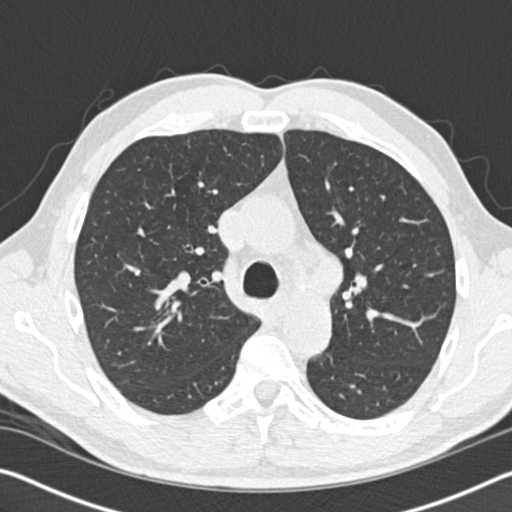
Axial slice from a low-dose chest CT screening exam; baseline annual screen; lung window (W 1500 / L -600 HU); standard (soft-tissue) reconstruction kernel (B30f); 512 × 512 image matrix, field of view 340 × 340 mm. Male participant, aged 61 years at enrolment. Former smoker at enrolment.
Expert-annotated lung lesion, bounding box (x1, y1, x2, y2) in pixels: (344, 276, 371, 313). The screening reader recorded 2 non-calcified nodules or masses ≥4 mm on this exam (right middle lobe, left upper lobe); which of them this box marks is not recorded. Later outcome: lung cancer diagnosed 183 days after this screen — small cell carcinoma, NOS, left upper lobe, stage IIIB (AJCC 6th edition), 100 mm at pathology.